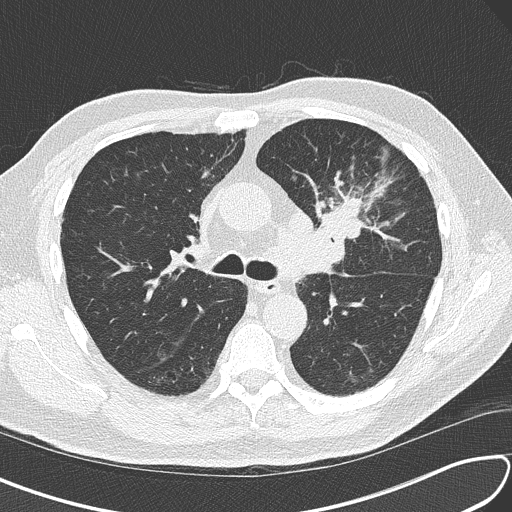
Chest CT (low-dose screening protocol), one axial image, third screening round (two years after baseline), lung window (W 1500 / L -600 HU), 2 mm slice thickness. Male participant, aged 67 years at enrolment. Current smoker at enrolment.
Lesion marked by an expert reader, bounding box <297,171,398,265> (left, top, right, bottom; pixels). Screening reader's record for this exam (one nodule recorded; not confirmed to be the boxed lesion): non-calcified nodule or mass ≥4 mm, left upper lobe, 30 × 23 mm, soft tissue attenuation, pre-existing on the prior screen: no. Official screen result: positive, other. Lung cancer was diagnosed 41 days after this screen: small cell carcinoma, NOS, left upper lobe, stage IV (AJCC 6th edition), 30 mm at pathology.